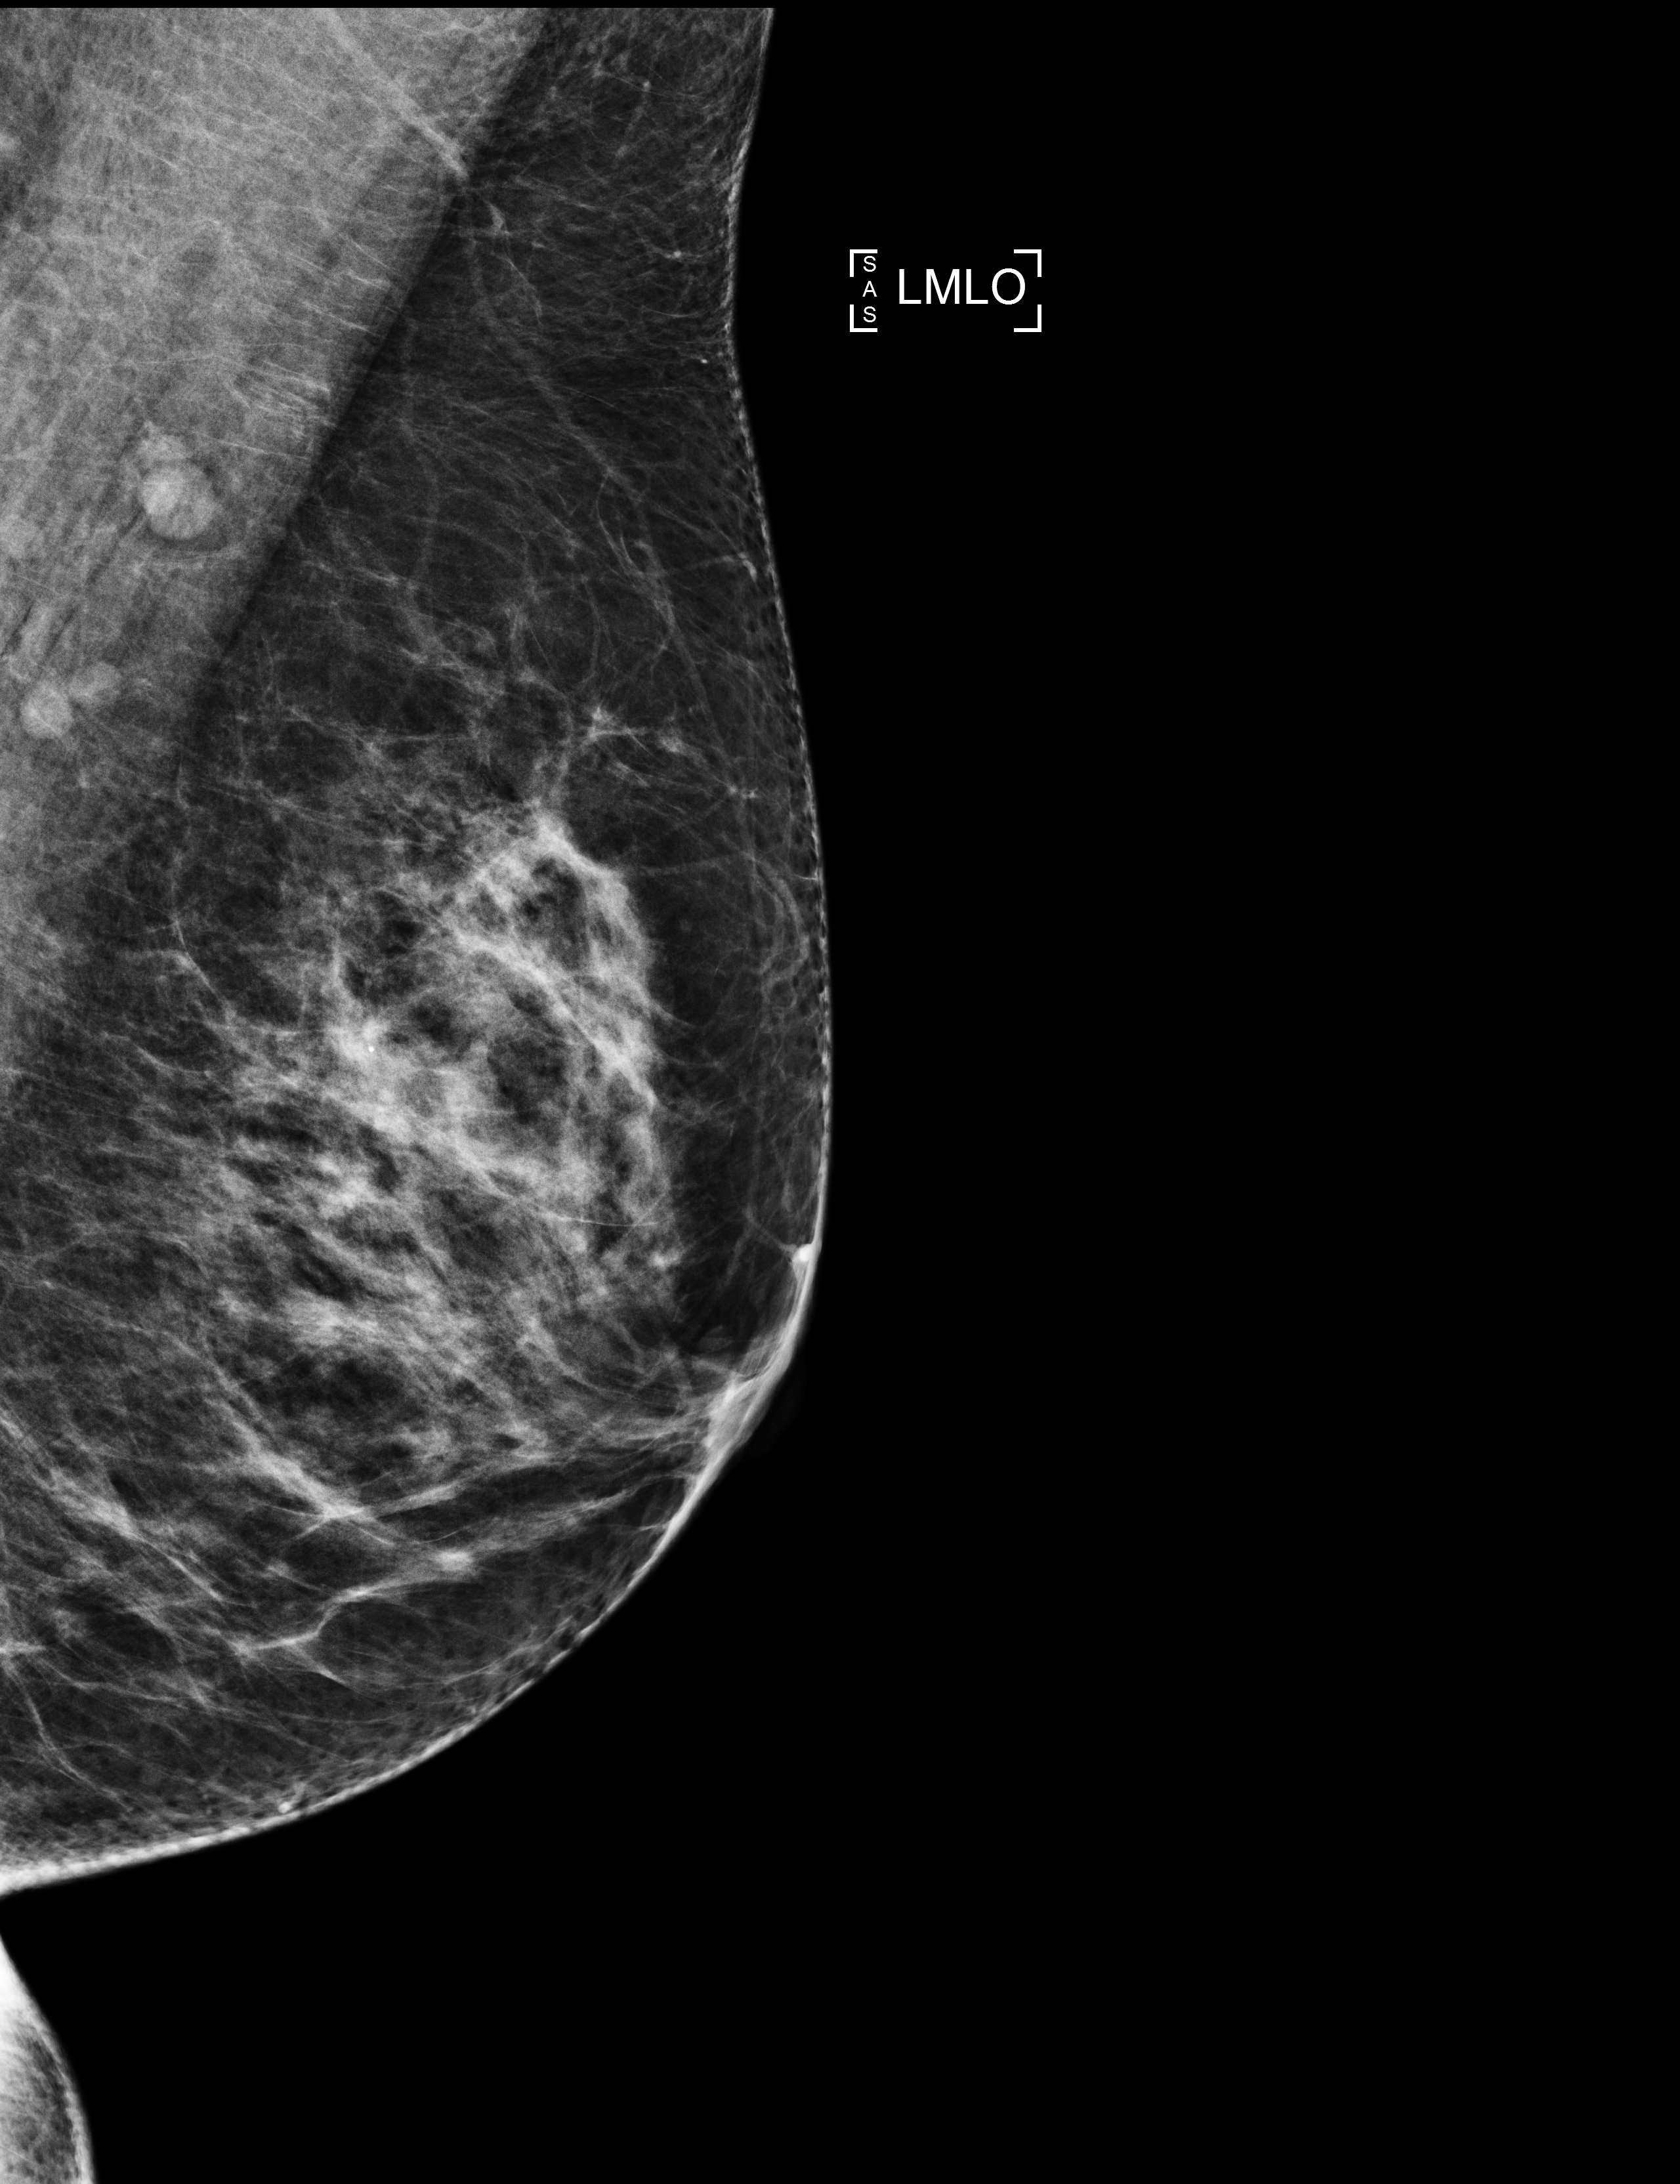
Full-field digital mammogram (FFDM), left breast, medio-lateral oblique projection, annual screening mammography examination, system: Selenia Dimensions. Patient: female, 54 years.
- breast density at the screening exam (both breasts): heterogeneously dense (BI-RADS density category c)
- final BI-RADS category for the screening round (tomosynthesis exam, both breasts): category 1
- recall: no recall after this screen